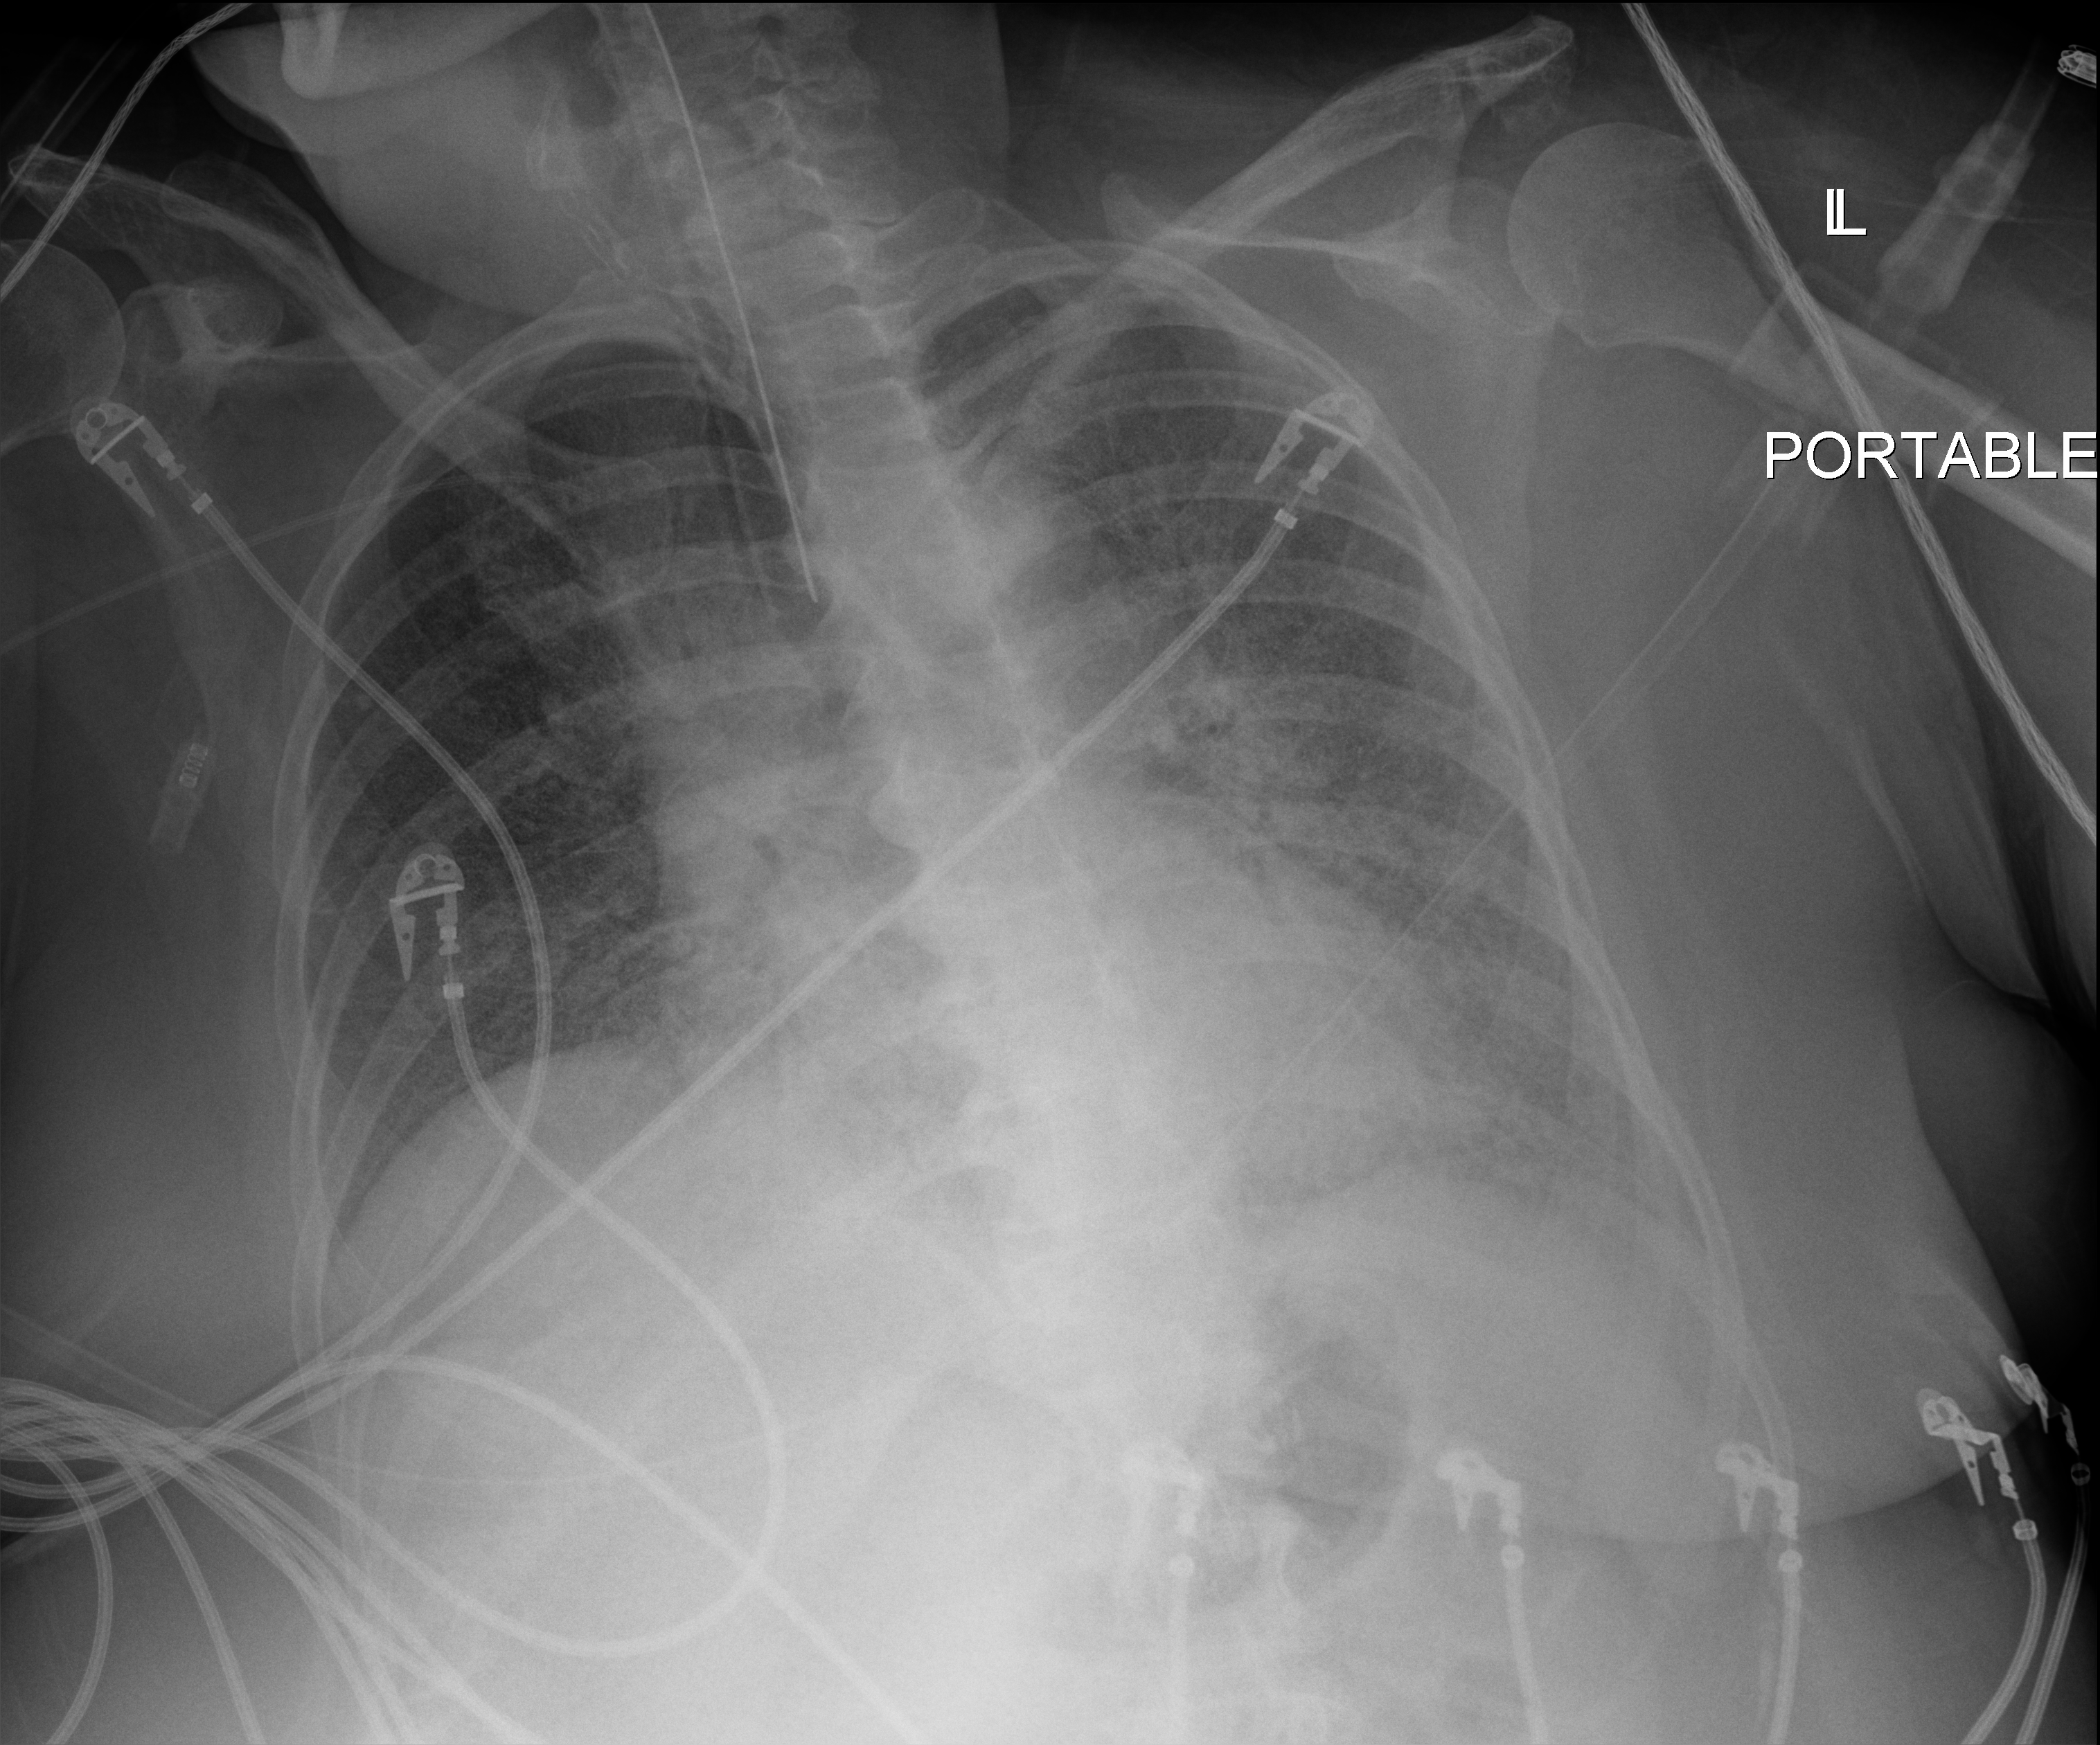
Portable chest radiograph; anteroposterior (AP) projection. Patient hospitalised with COVID-19; female, aged 60–74 years.
Admission-level facts for this patient (not findings on this image; timing relative to this image not recorded): admitted to intensive care during this hospital stay: yes; mechanically ventilated during this hospital stay: yes.